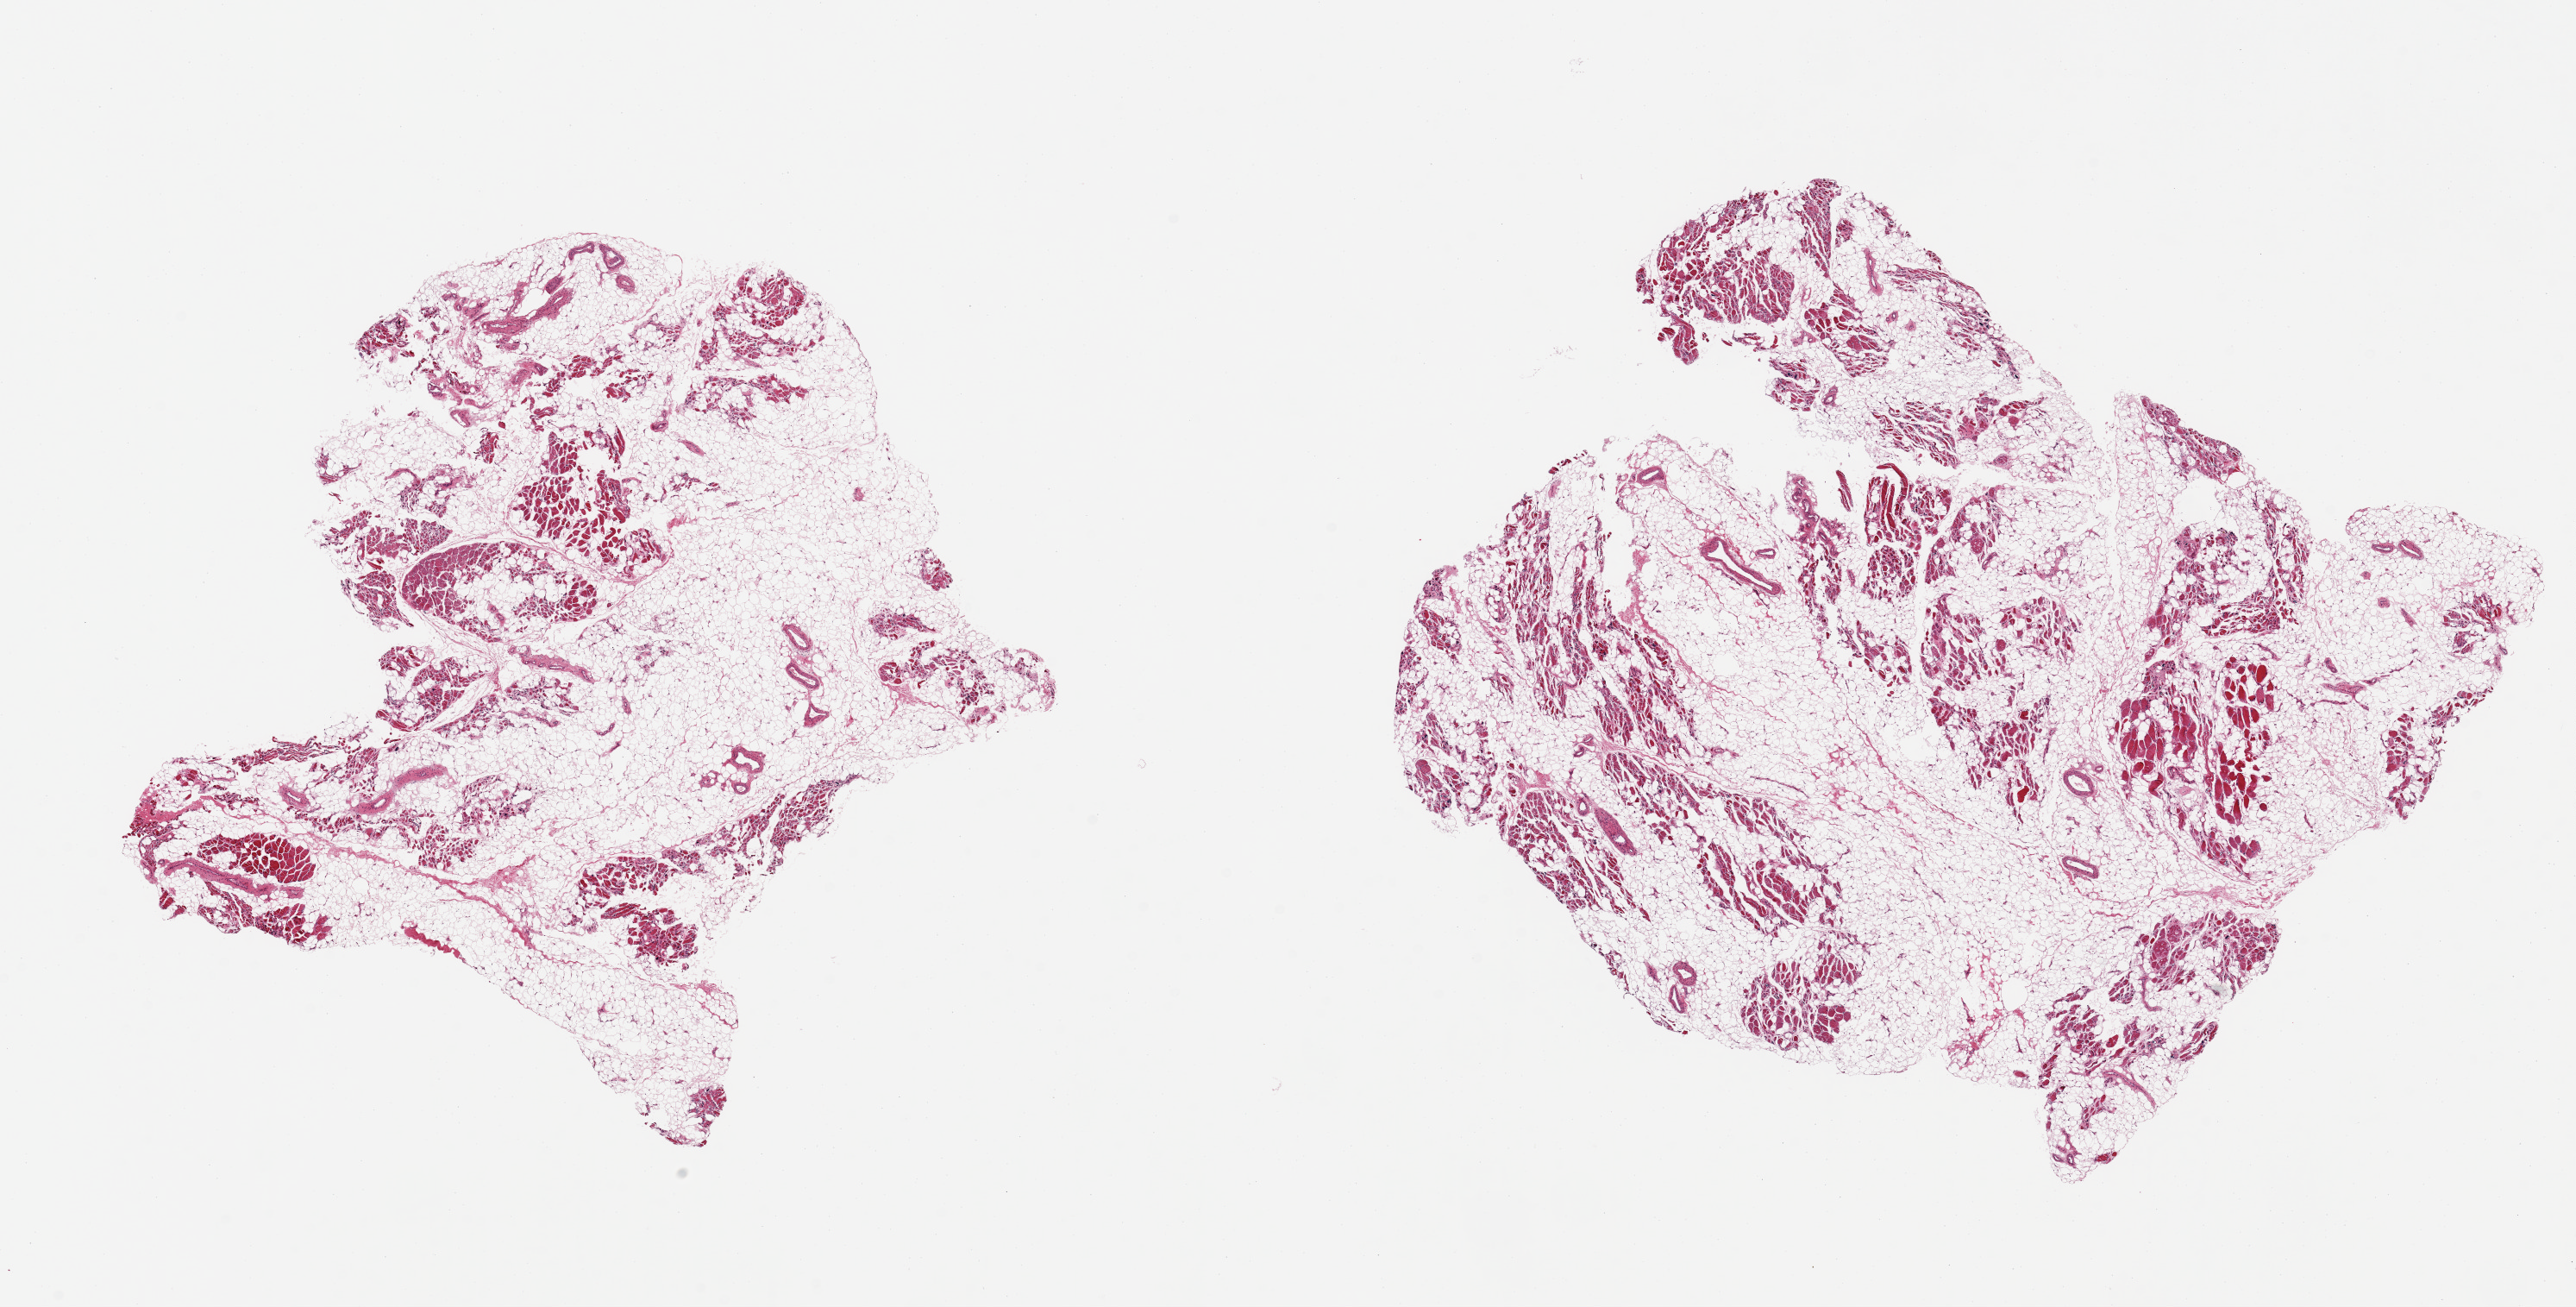
Whole-slide image, hematoxylin and eosin (H&E) stain — shown as a low-resolution overview of the whole scanned area (about 23.6 x 12.0 mm). PAXgene-fixed paraffin-embedded (PFPE) section. Sampled site (target tissue): skeletal muscle. Donor tissue sample. Male donor.
- pathologist's review note for this sample: 2 pieces, marked atrophy with fatty infiltration